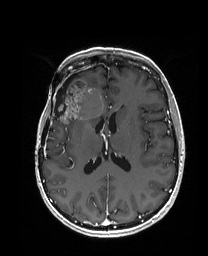
Brain MRI from a brain-tumour surgery series, one axial slice; position 83 of 192 along the scan axis; T1-weighted post-contrast; 208 × 256 image matrix, field of view 203 × 250 mm. From the clinical record (not read from this slice): histopathology: Metastatic Carcinoma from Breast primary; tumour location: Right Frontal.
Outlined on this slice (expert manual segmentation):
- previous resection cavity: bounding box <55,77,72,116> (left, top, right, bottom; pixels)
- tumour: <55,79,104,124>